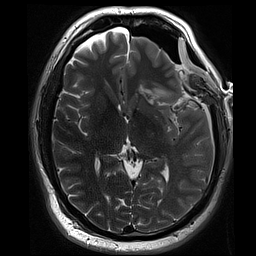
Brain MRI from a brain-tumour surgery series, one axial slice; 2 mm slice thickness; 256 × 256 image matrix, field of view 220 × 220 mm. From the clinical record (not read from this slice): histopathology: Oligodendroglioma; WHO grade: 3; IDH mutation: yes.
Annotated regions visible in this slice (outlined manually by an expert reader):
- residual tumour: bounding box <144,88,177,106> (left, top, right, bottom; pixels)